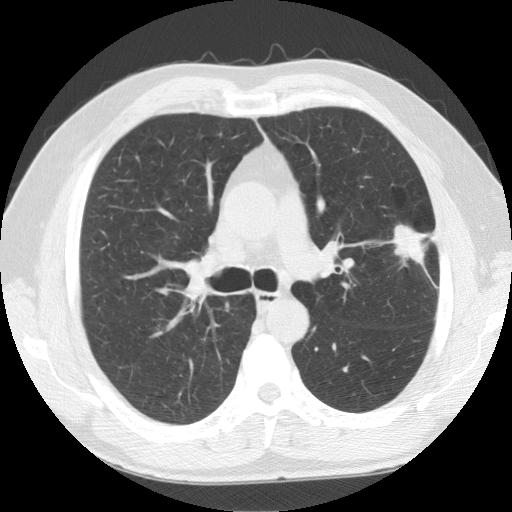
Low-dose screening chest CT, one axial slice; position 94 of 141 along the scan axis; lung window (W 1500 / L -600 HU); 2.5 mm slice thickness; 512 × 512 image matrix.
Annotated regions visible in this slice (expert manual segmentation):
- lesion 1 (tumor, upper lobe of left lung): bounding box (x1, y1, x2, y2) in pixels: (391, 225, 427, 265)